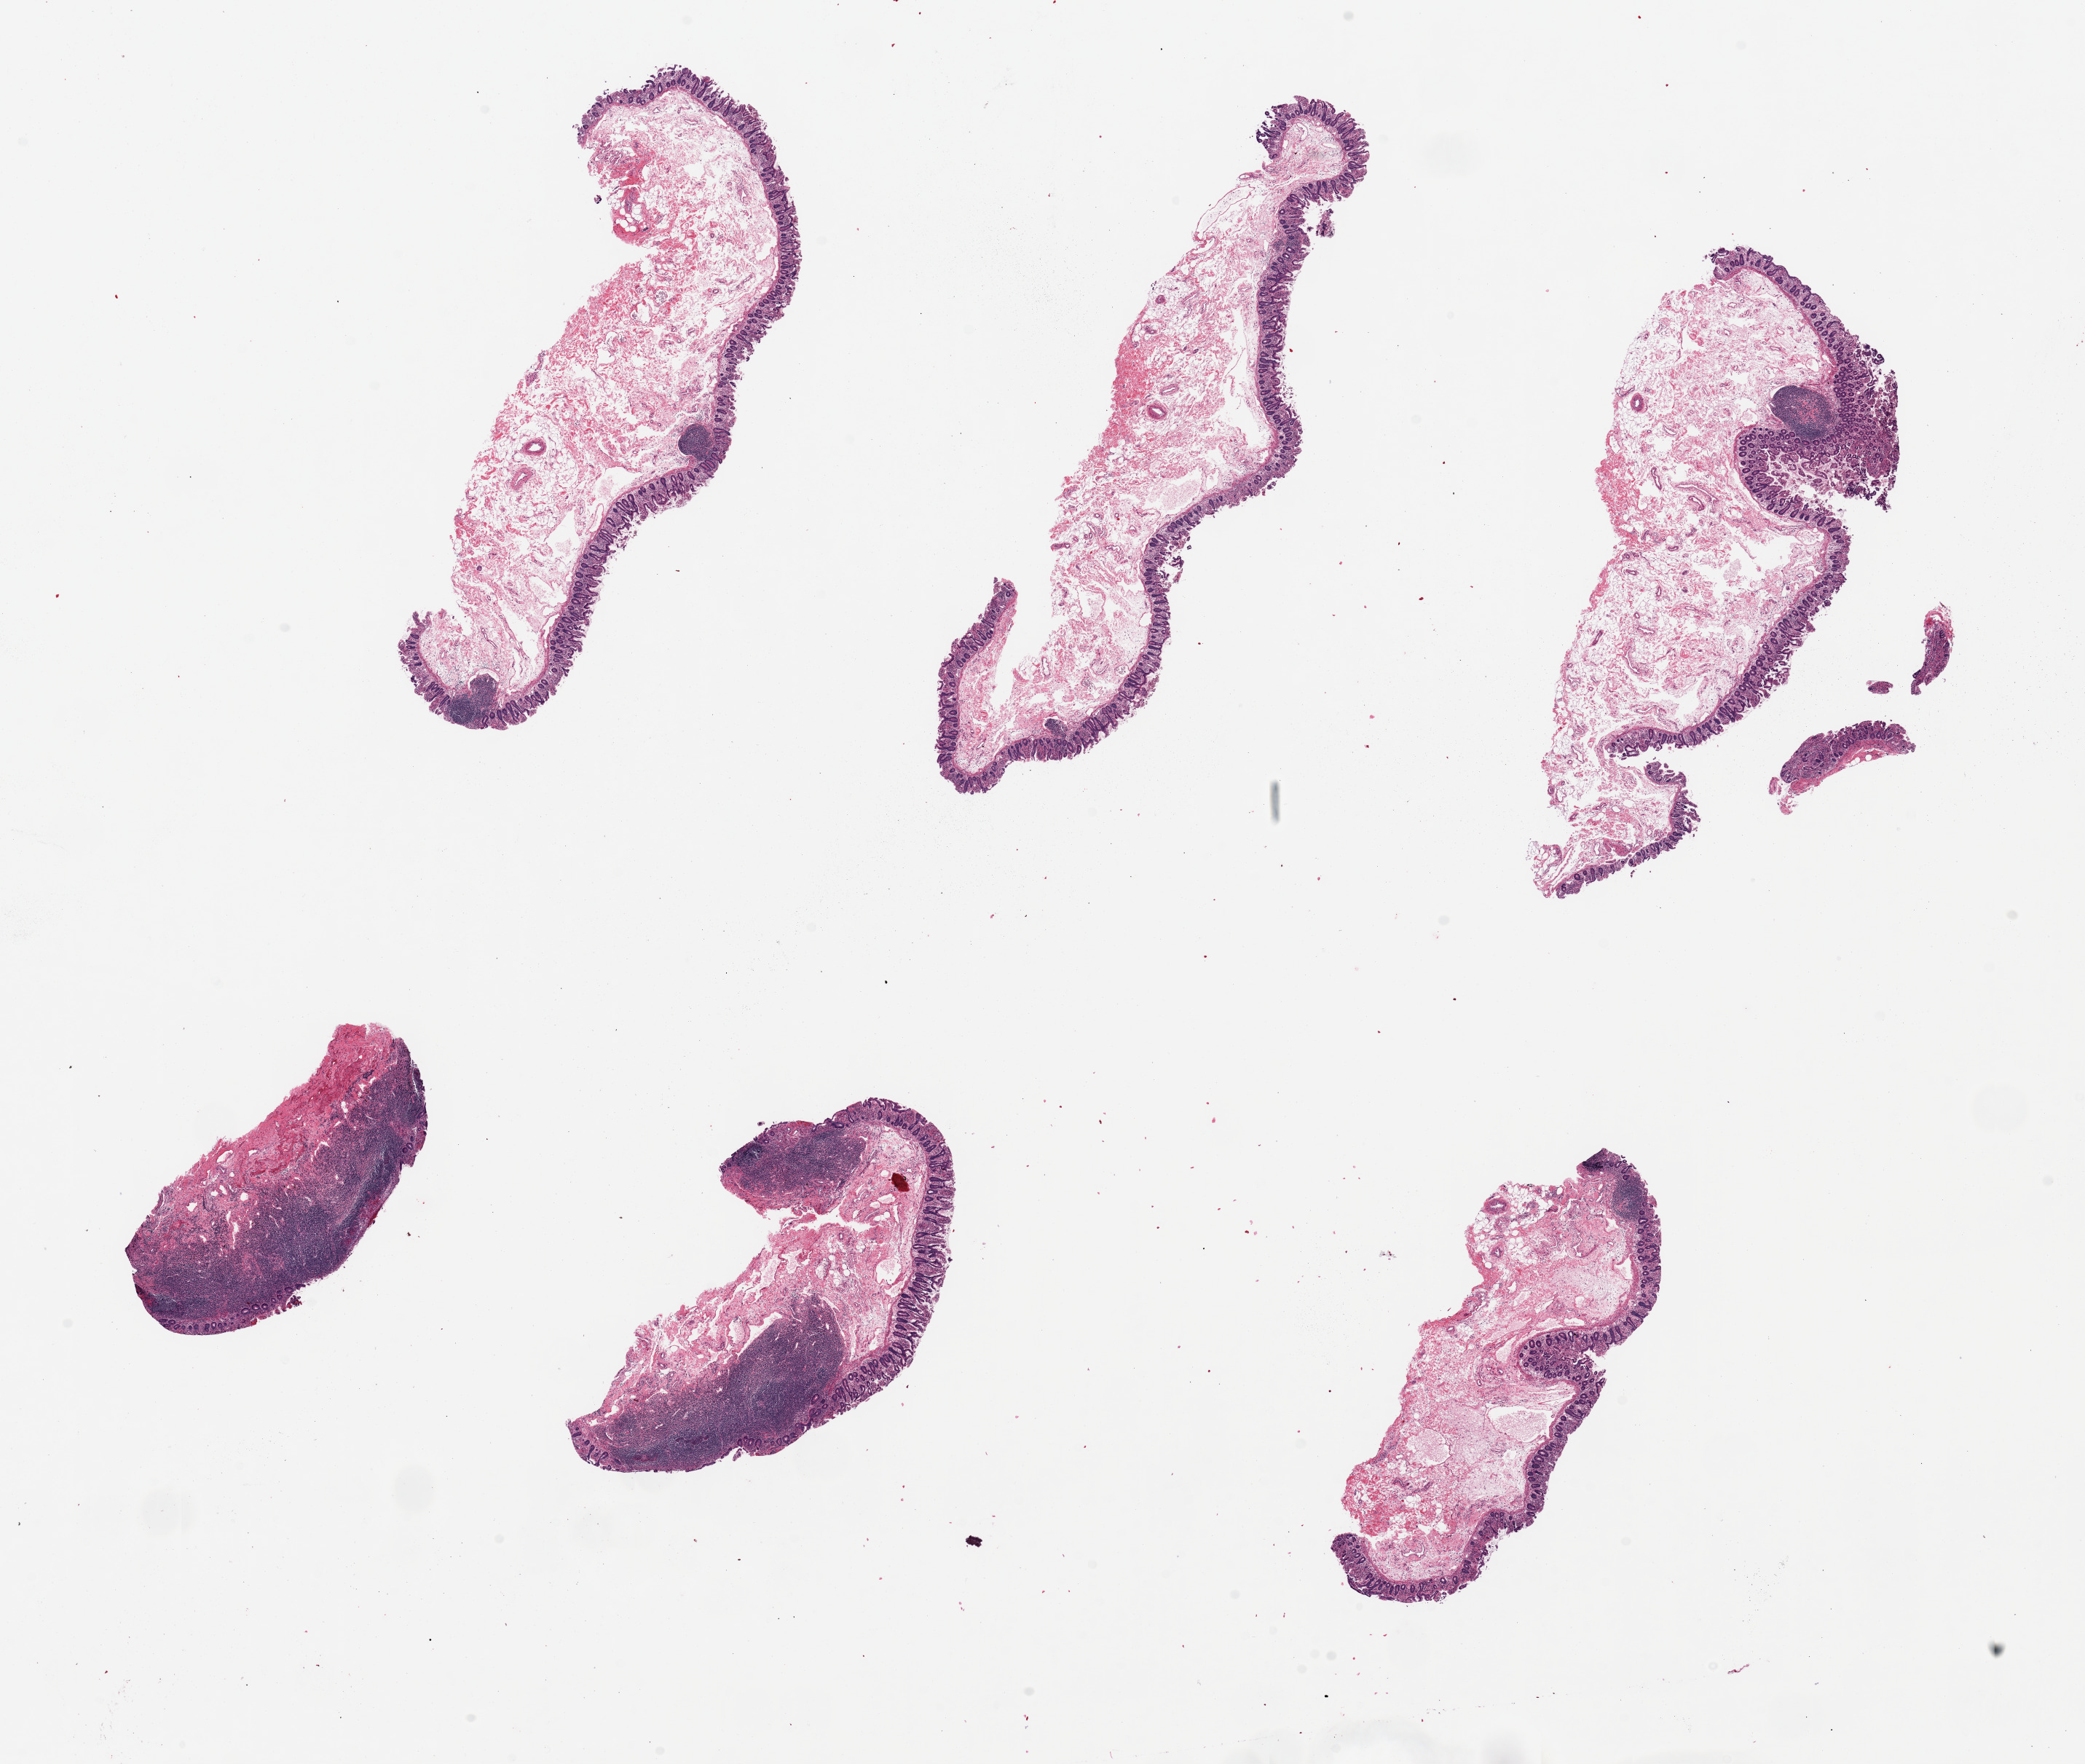
Digitized hematoxylin and eosin (H&E)-stained section, shown as a low-resolution overview of the whole scanned area (about 22.6 x 19.2 mm, slide scanned at 20x); PAXgene-fixed paraffin-embedded (PFPE) section; target tissue: ileum; donor tissue sample. Donor: male.
Pathologist's review note for this sample: 6 pieces, ~7x2mm minimal muscle; only 2 have significant lymphoid cells; Abundant fat/mucosa in 5.